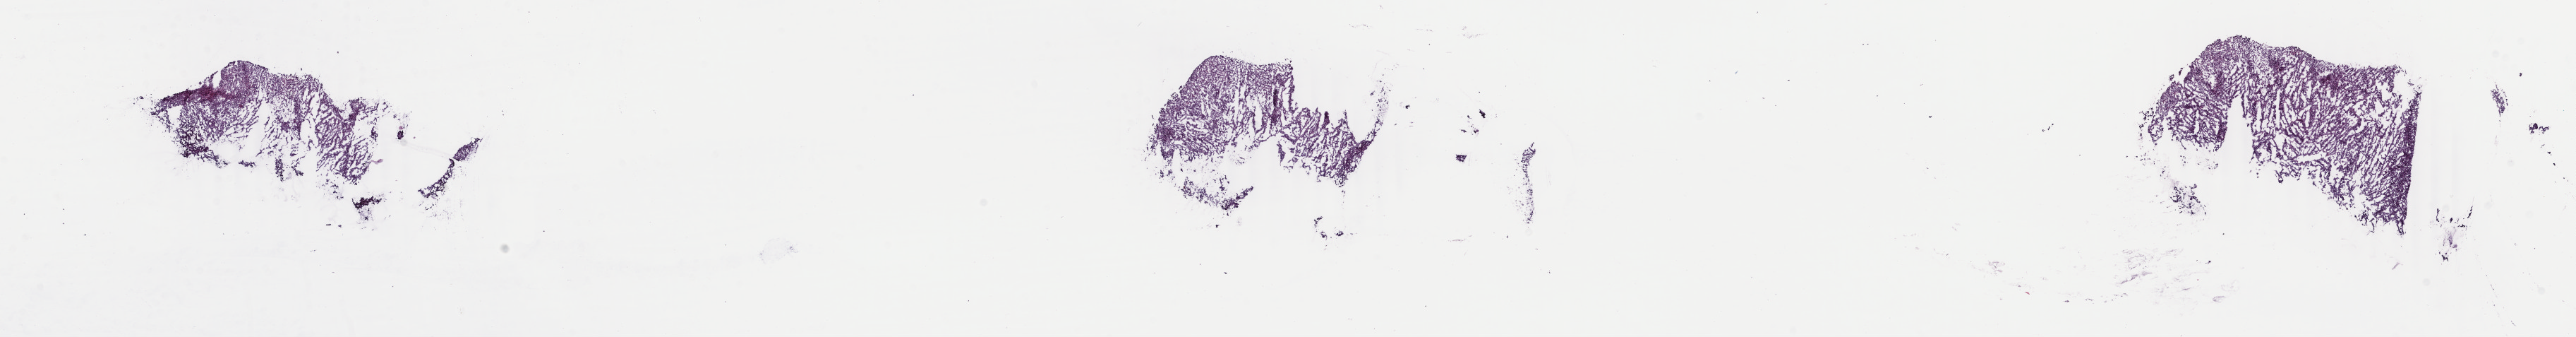
H&E whole-slide image, low-resolution overview of the scanned area, about 29.0 x 3.8 mm, frozen section from the top of the tissue portion, adrenal cortex, primary tumour sample. Patient: male, age at initial diagnosis 63 years. Pathologist review of this section (percent, as recorded): tumour cells 100%, tumour nuclei 80%, normal cells 0%, stromal cells 0%, necrosis 0%. Infiltration values recorded for this section: lymphocyte infiltration 1%, monocyte infiltration 0%, neutrophil infiltration 0%.
- diagnosis: Adrenal cortical carcinoma
- laterality: left